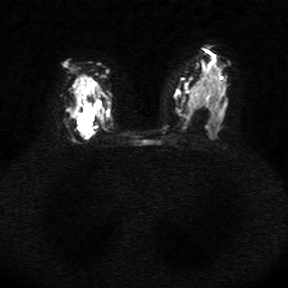
Breast MRI, one axial slice; diffusion-weighted series; image 2 of 4 stored at this slice position (different b-values; order by instance number); 1.5 T; 288 × 288 image matrix, field of view 340 × 340 mm. Female patient.
Outlined on this slice (expert manual segmentation):
- tumour on diffusion-weighted imaging: box from (x=75, y=107) to (x=93, y=135) px